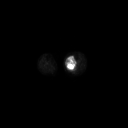
FDG PET of an extremity soft-tissue mass (from a PET/CT study), one axial slice; 128 × 128 image matrix, field of view 700 × 700 mm. Patient: female, 70 years. From the clinical record (not read from this slice): histological type: extraskeletal high grade osteogenic sarcoma; grade: high; site of the primary tumour: left calf.
Structures marked on this image (expert contour drawn on MRI and transferred to this co-registered scan by the dataset authors):
- gross tumour volume (mass): box from (x=66, y=57) to (x=76, y=70) px